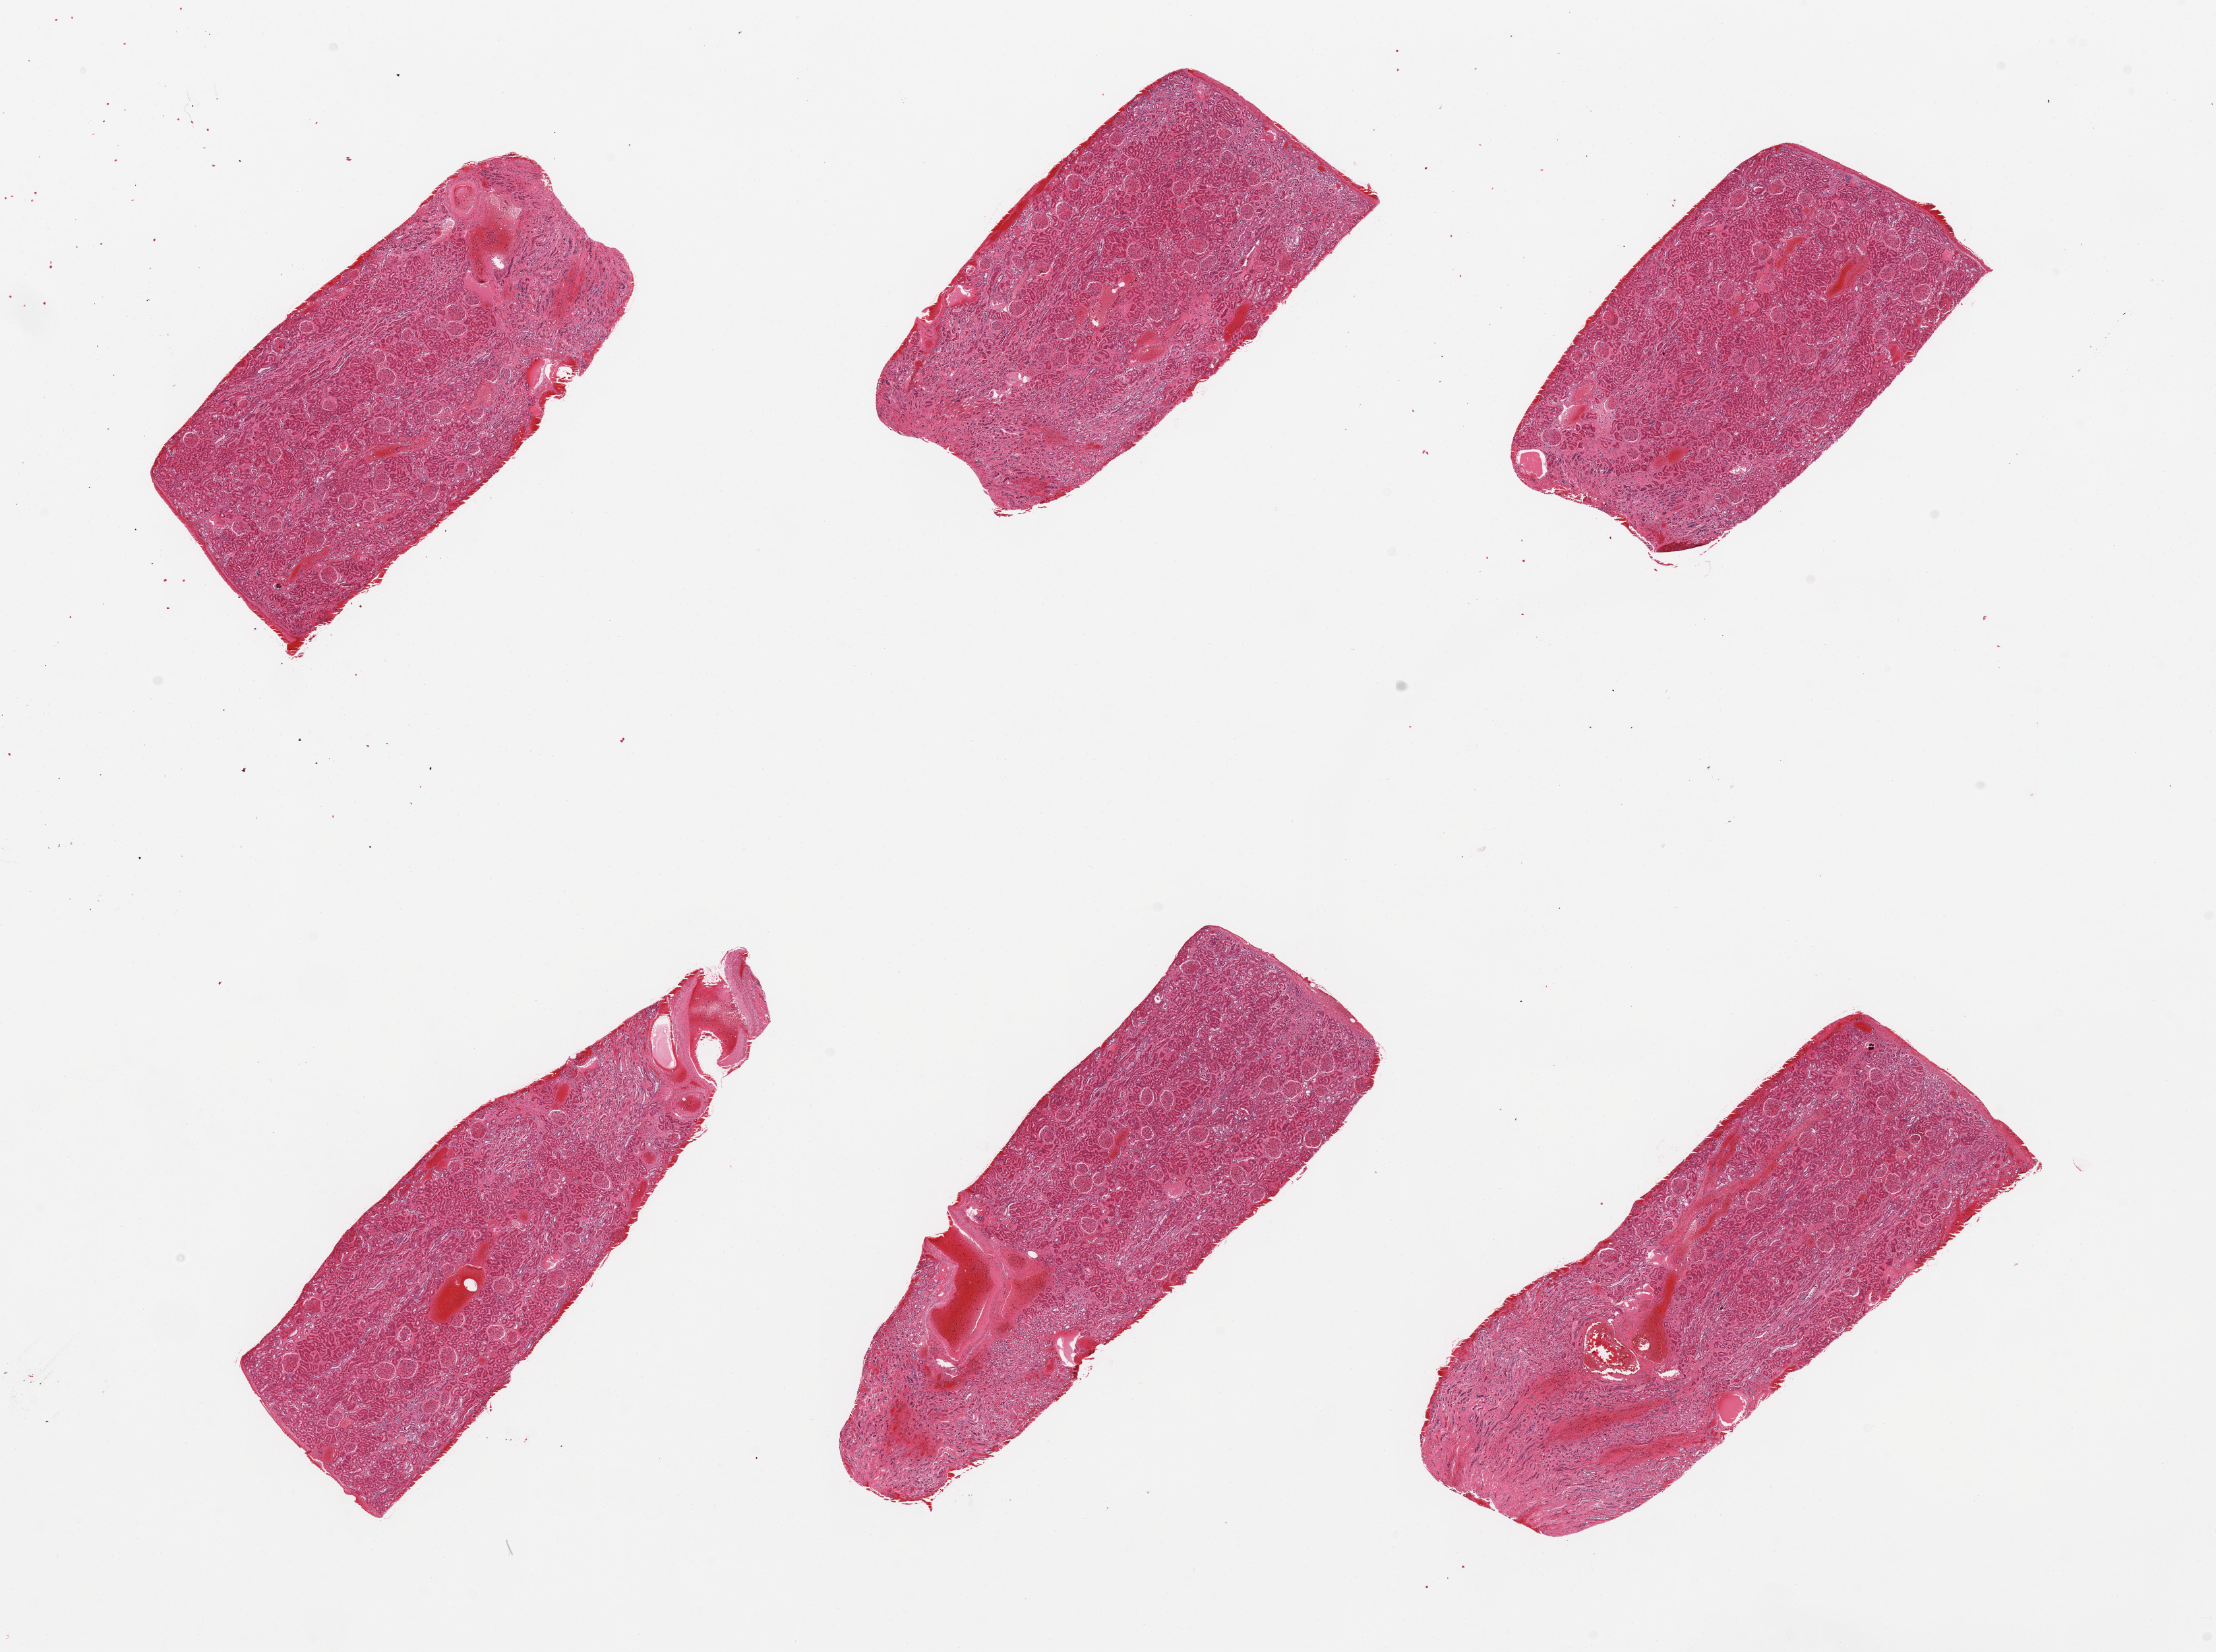
Whole-slide image, H&E stain, brightfield — whole scanned area (about 26.6 x 19.8 mm, acquisition: 20x scan) shown as a low-resolution overview, PAXgene-fixed, paraffin-embedded tissue, section of renal cortex (target tissue), tissue donor sample. Donor sex: female.
Pathologist's review note for this sample: 6 pieces, glomeruli present, all sections.